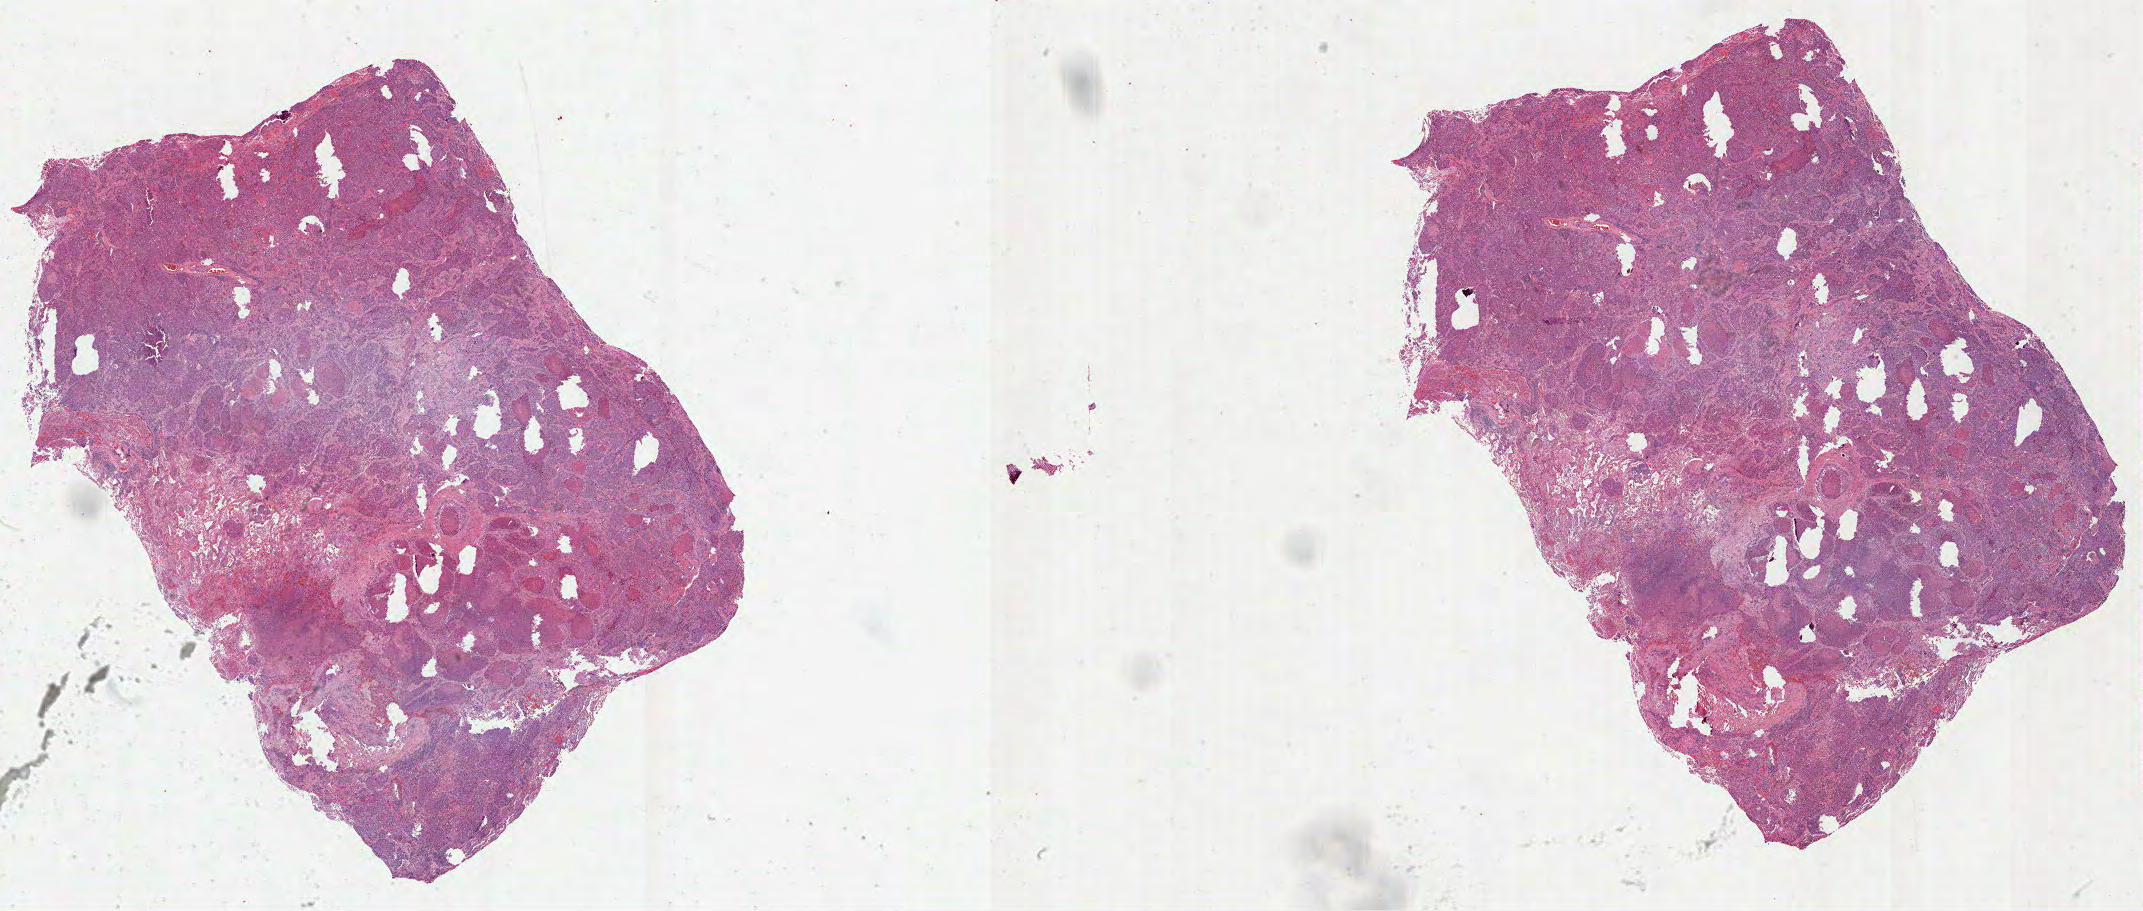
Whole-slide histology image, H&E-stained — shown as a low-resolution overview of the whole scanned area (about 34.6 x 14.7 mm), formalin-fixed paraffin-embedded (FFPE) diagnostic section, primary tumour sample from the lung. Male patient; age at initial diagnosis 76 years.
* TNM: T2 N1 MX
* AJCC pathologic stage: IIB (6th edition)
* histologic diagnosis: Squamous cell carcinoma, NOS (middle lobe, lung)
* laterality: right